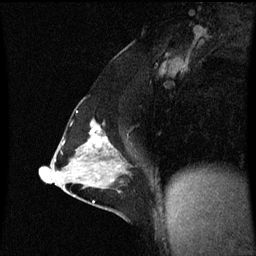
Breast MRI (dynamic contrast-enhanced), one sagittal slice; position 33 of 60 along the scan axis; dynamic contrast-enhanced series, image 2 of 3 at this slice position (ordered by acquisition); 1.5 T; TE 4.2 ms, TR 8.9 ms; 256 × 256 image matrix. Female patient, age 47 years. Case-level facts recorded for this patient, not image findings: setting: breast cancer imaged before/during neoadjuvant chemotherapy; receptor status: HR-positive, HER2-negative.
Annotated regions visible in this slice (semi-automatically segmented with operator editing):
- analysis volume of interest (the breast-tissue region the enhancement analysis was run in; not a lesion): bounding box (x1, y1, x2, y2) in pixels: (53, 110, 131, 209)
- tumour enhancement mask (voxels above the 70 % enhancement threshold inside the analysis volume of interest): (85, 124, 120, 167)